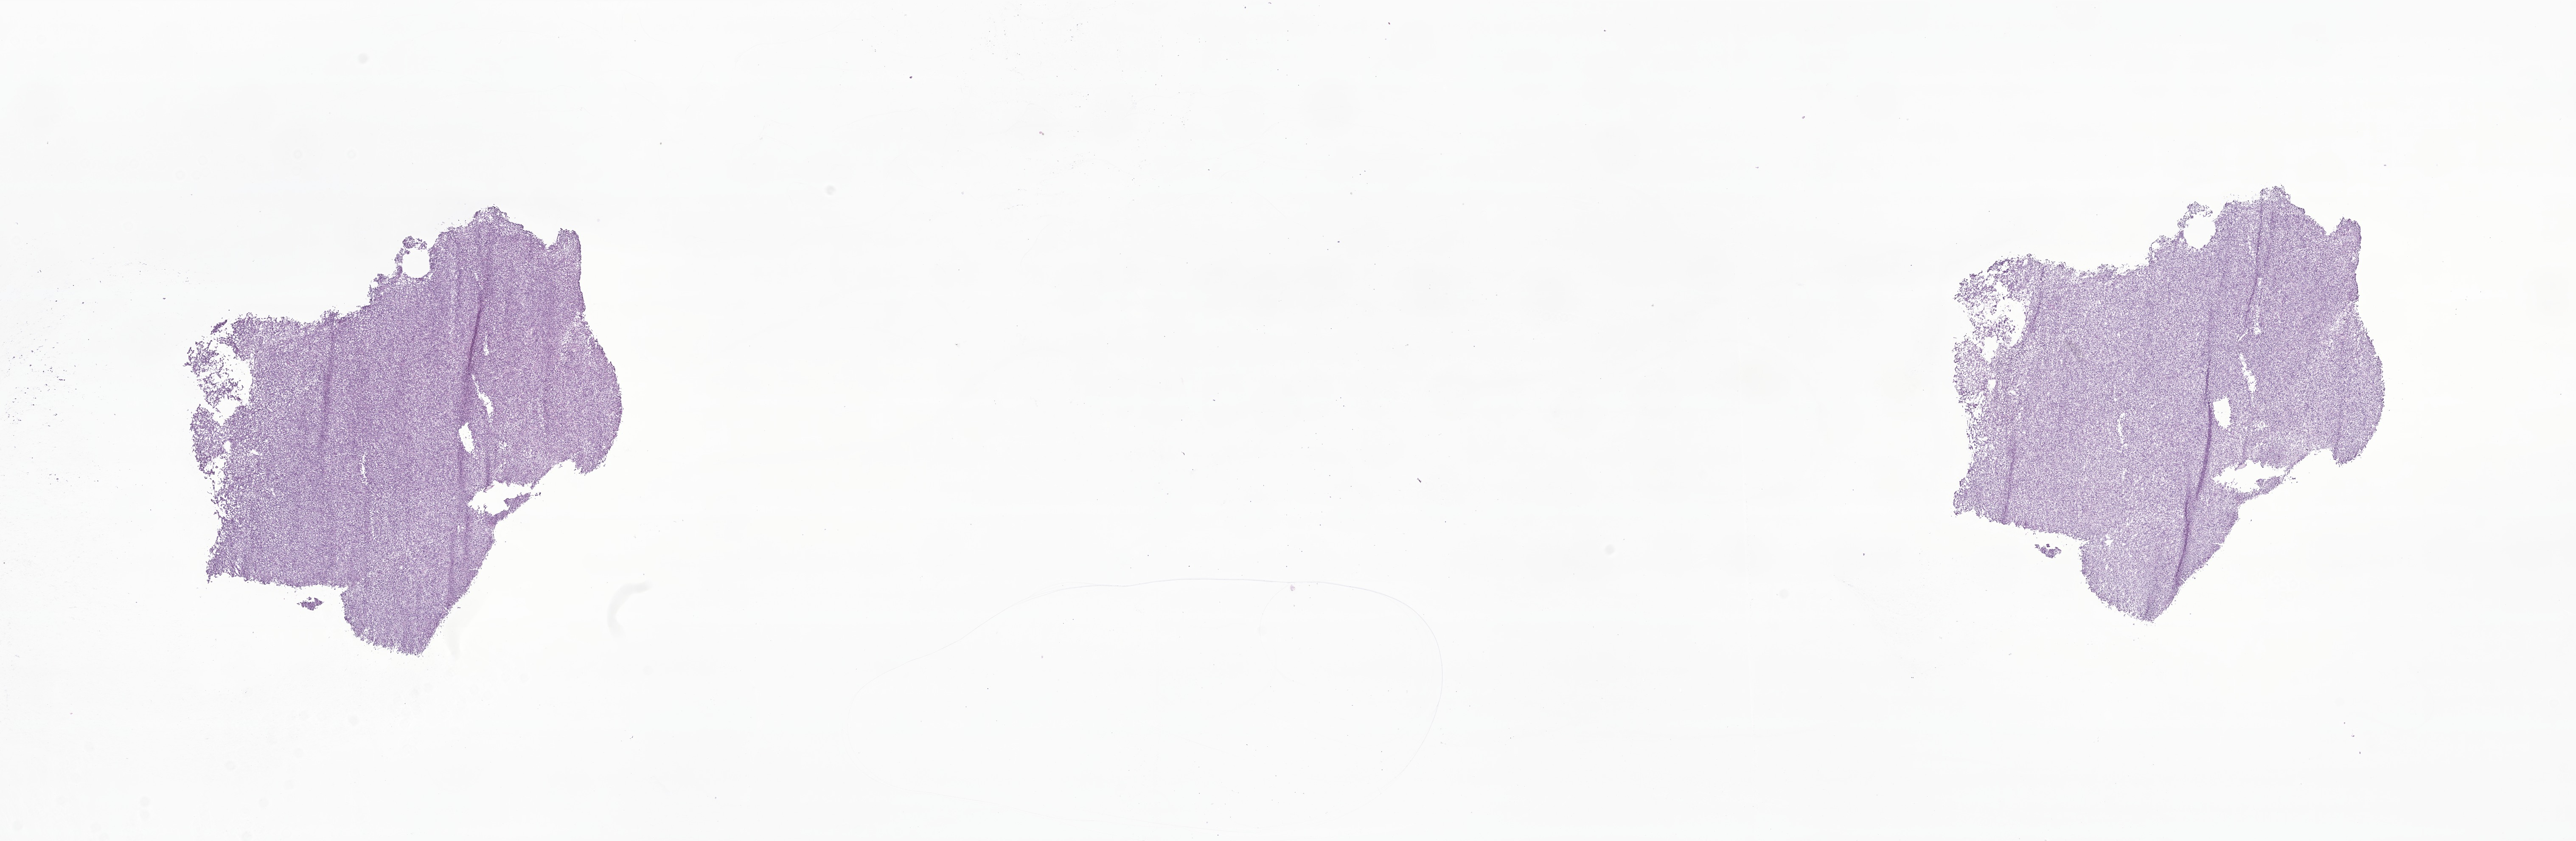
H&E whole-slide image of tumor tissue from the brain — low-resolution overview of the scanned area, about 25.6 x 8.4 mm, cryosection (OCT / tissue freezing medium). Female patient, age 166 months (13 years 10 months).
* recorded diagnosis: Oligoastrocytoma, NOS